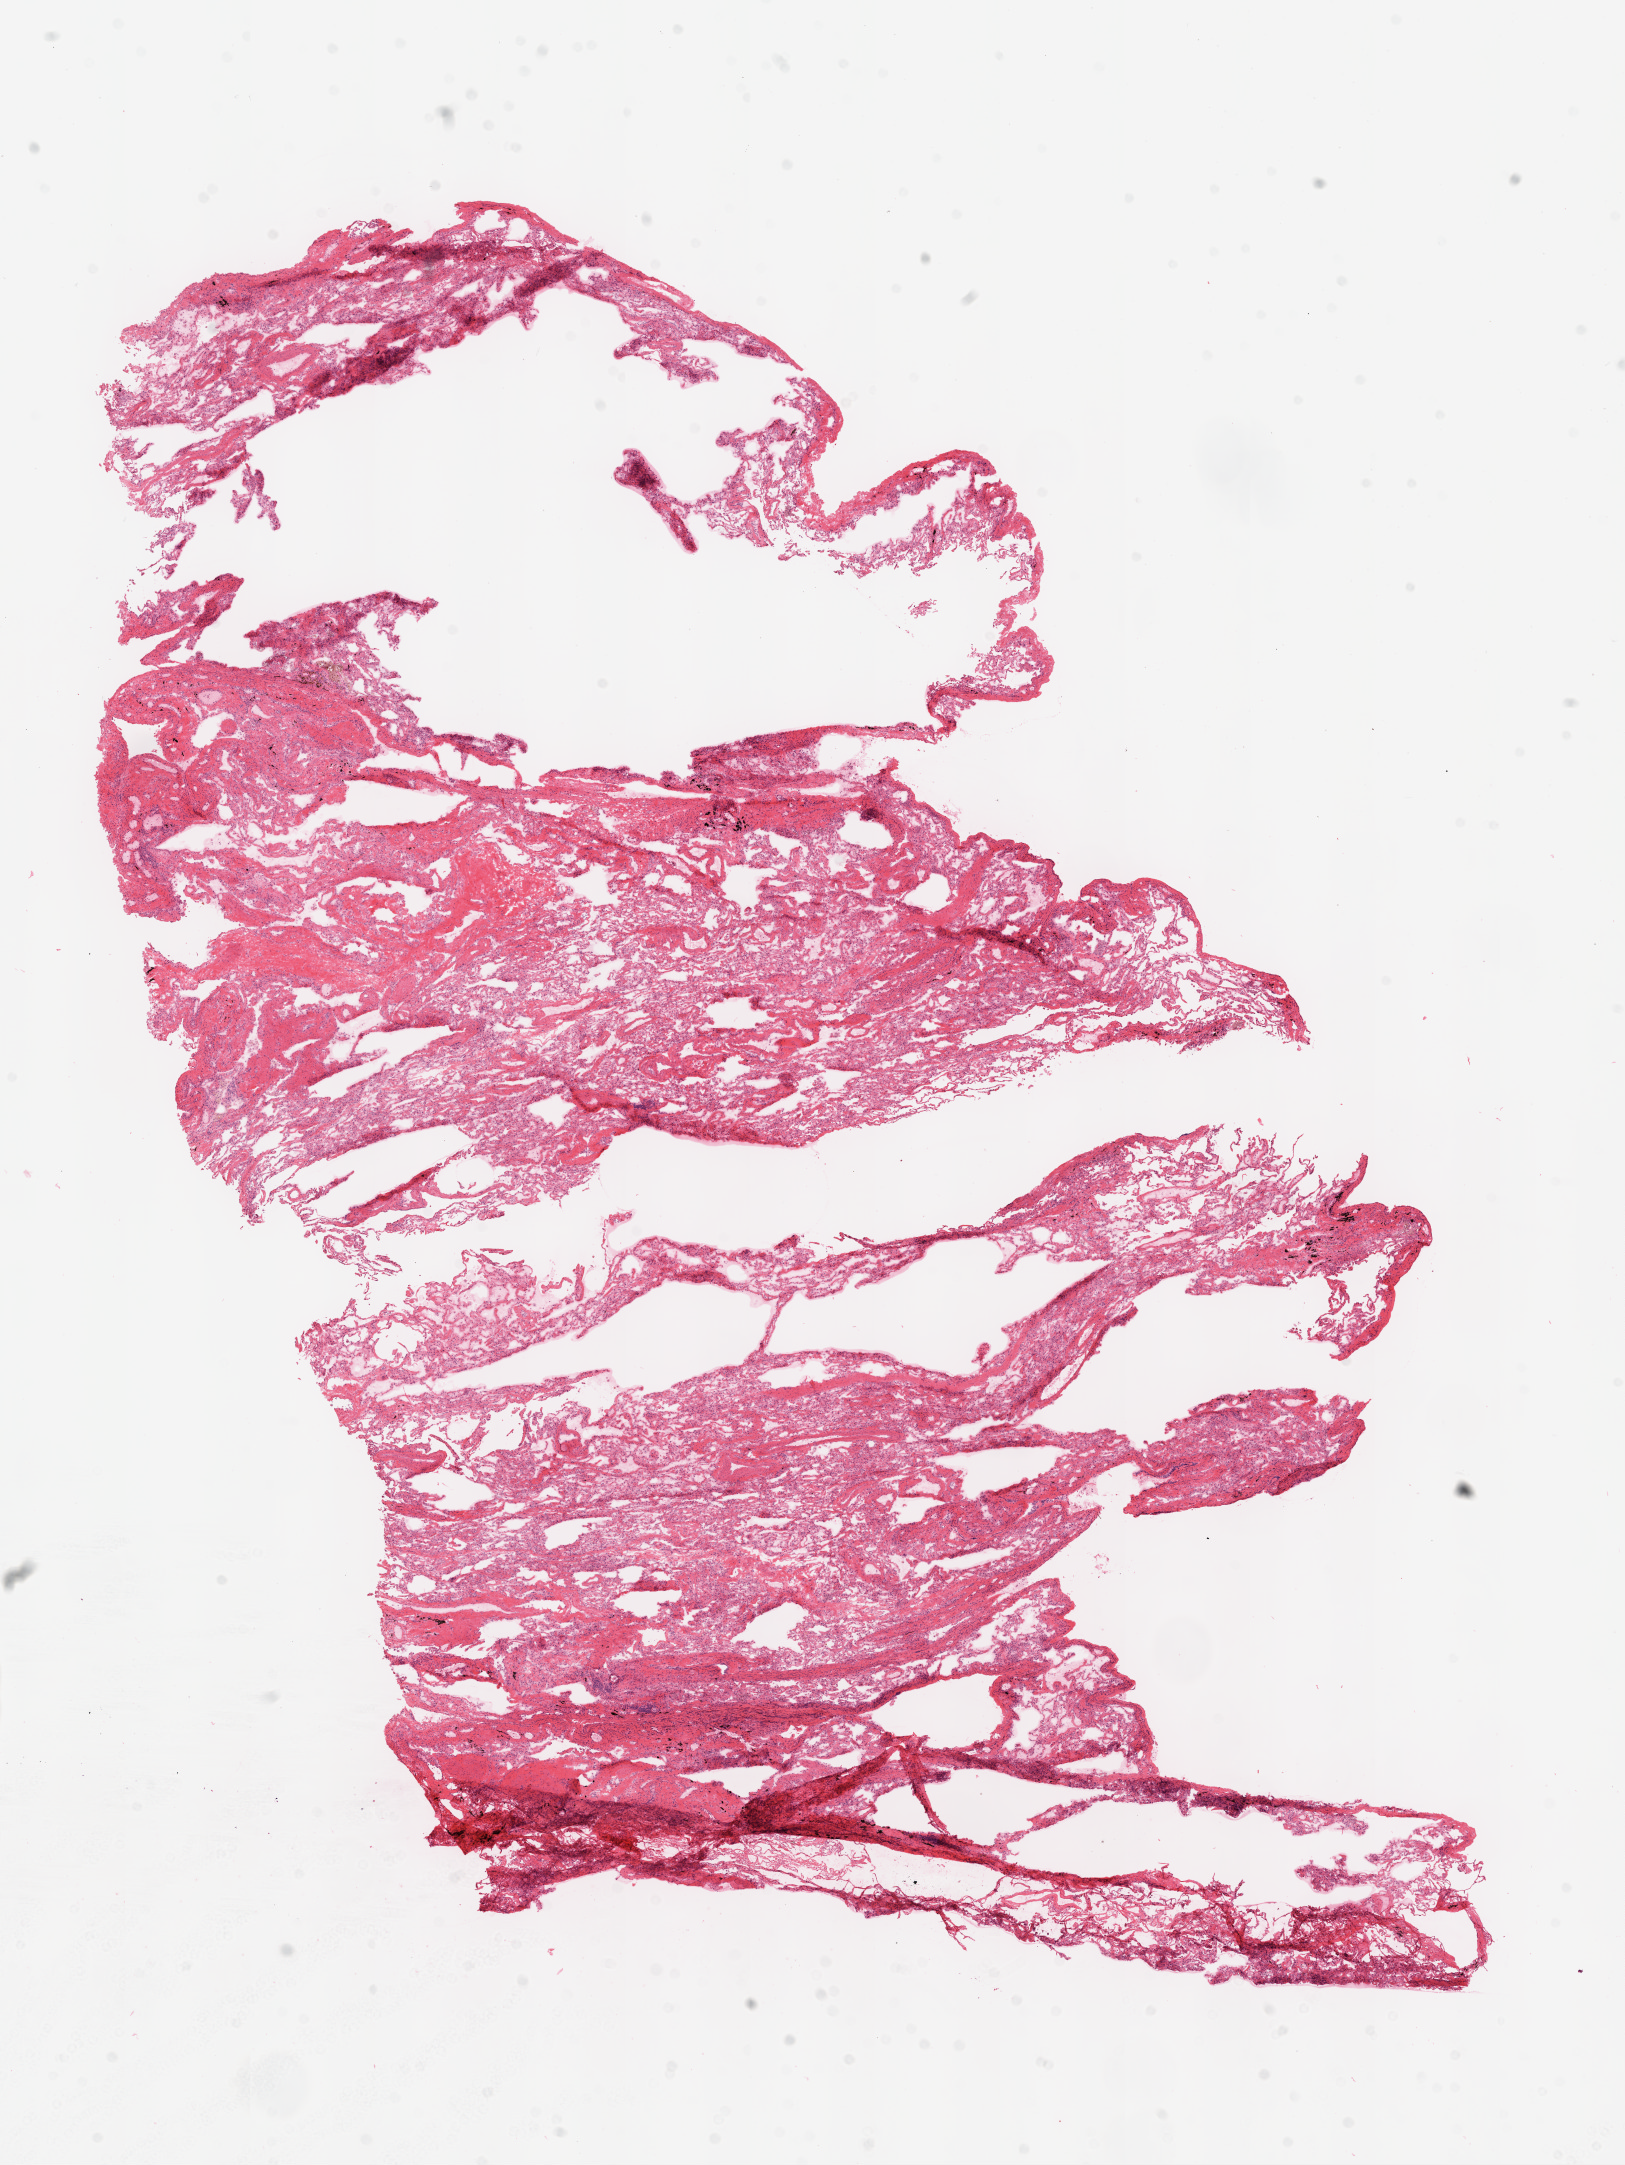
Digitized Hematoxylin and eosin (H&E) stained tissue section (whole slide), a low-resolution overview of the entire scanned area, about 13.0 x 17.4 mm (from a 20x scan). Frozen section from the top of the tissue portion. Sample: solid tissue normal (non-tumour tissue), lung. Male, age 59 years at initial diagnosis.
This section: solid tissue normal sample (biorepository sample class). Patient diagnosis: Squamous cell carcinoma, NOS (upper lobe, lung).